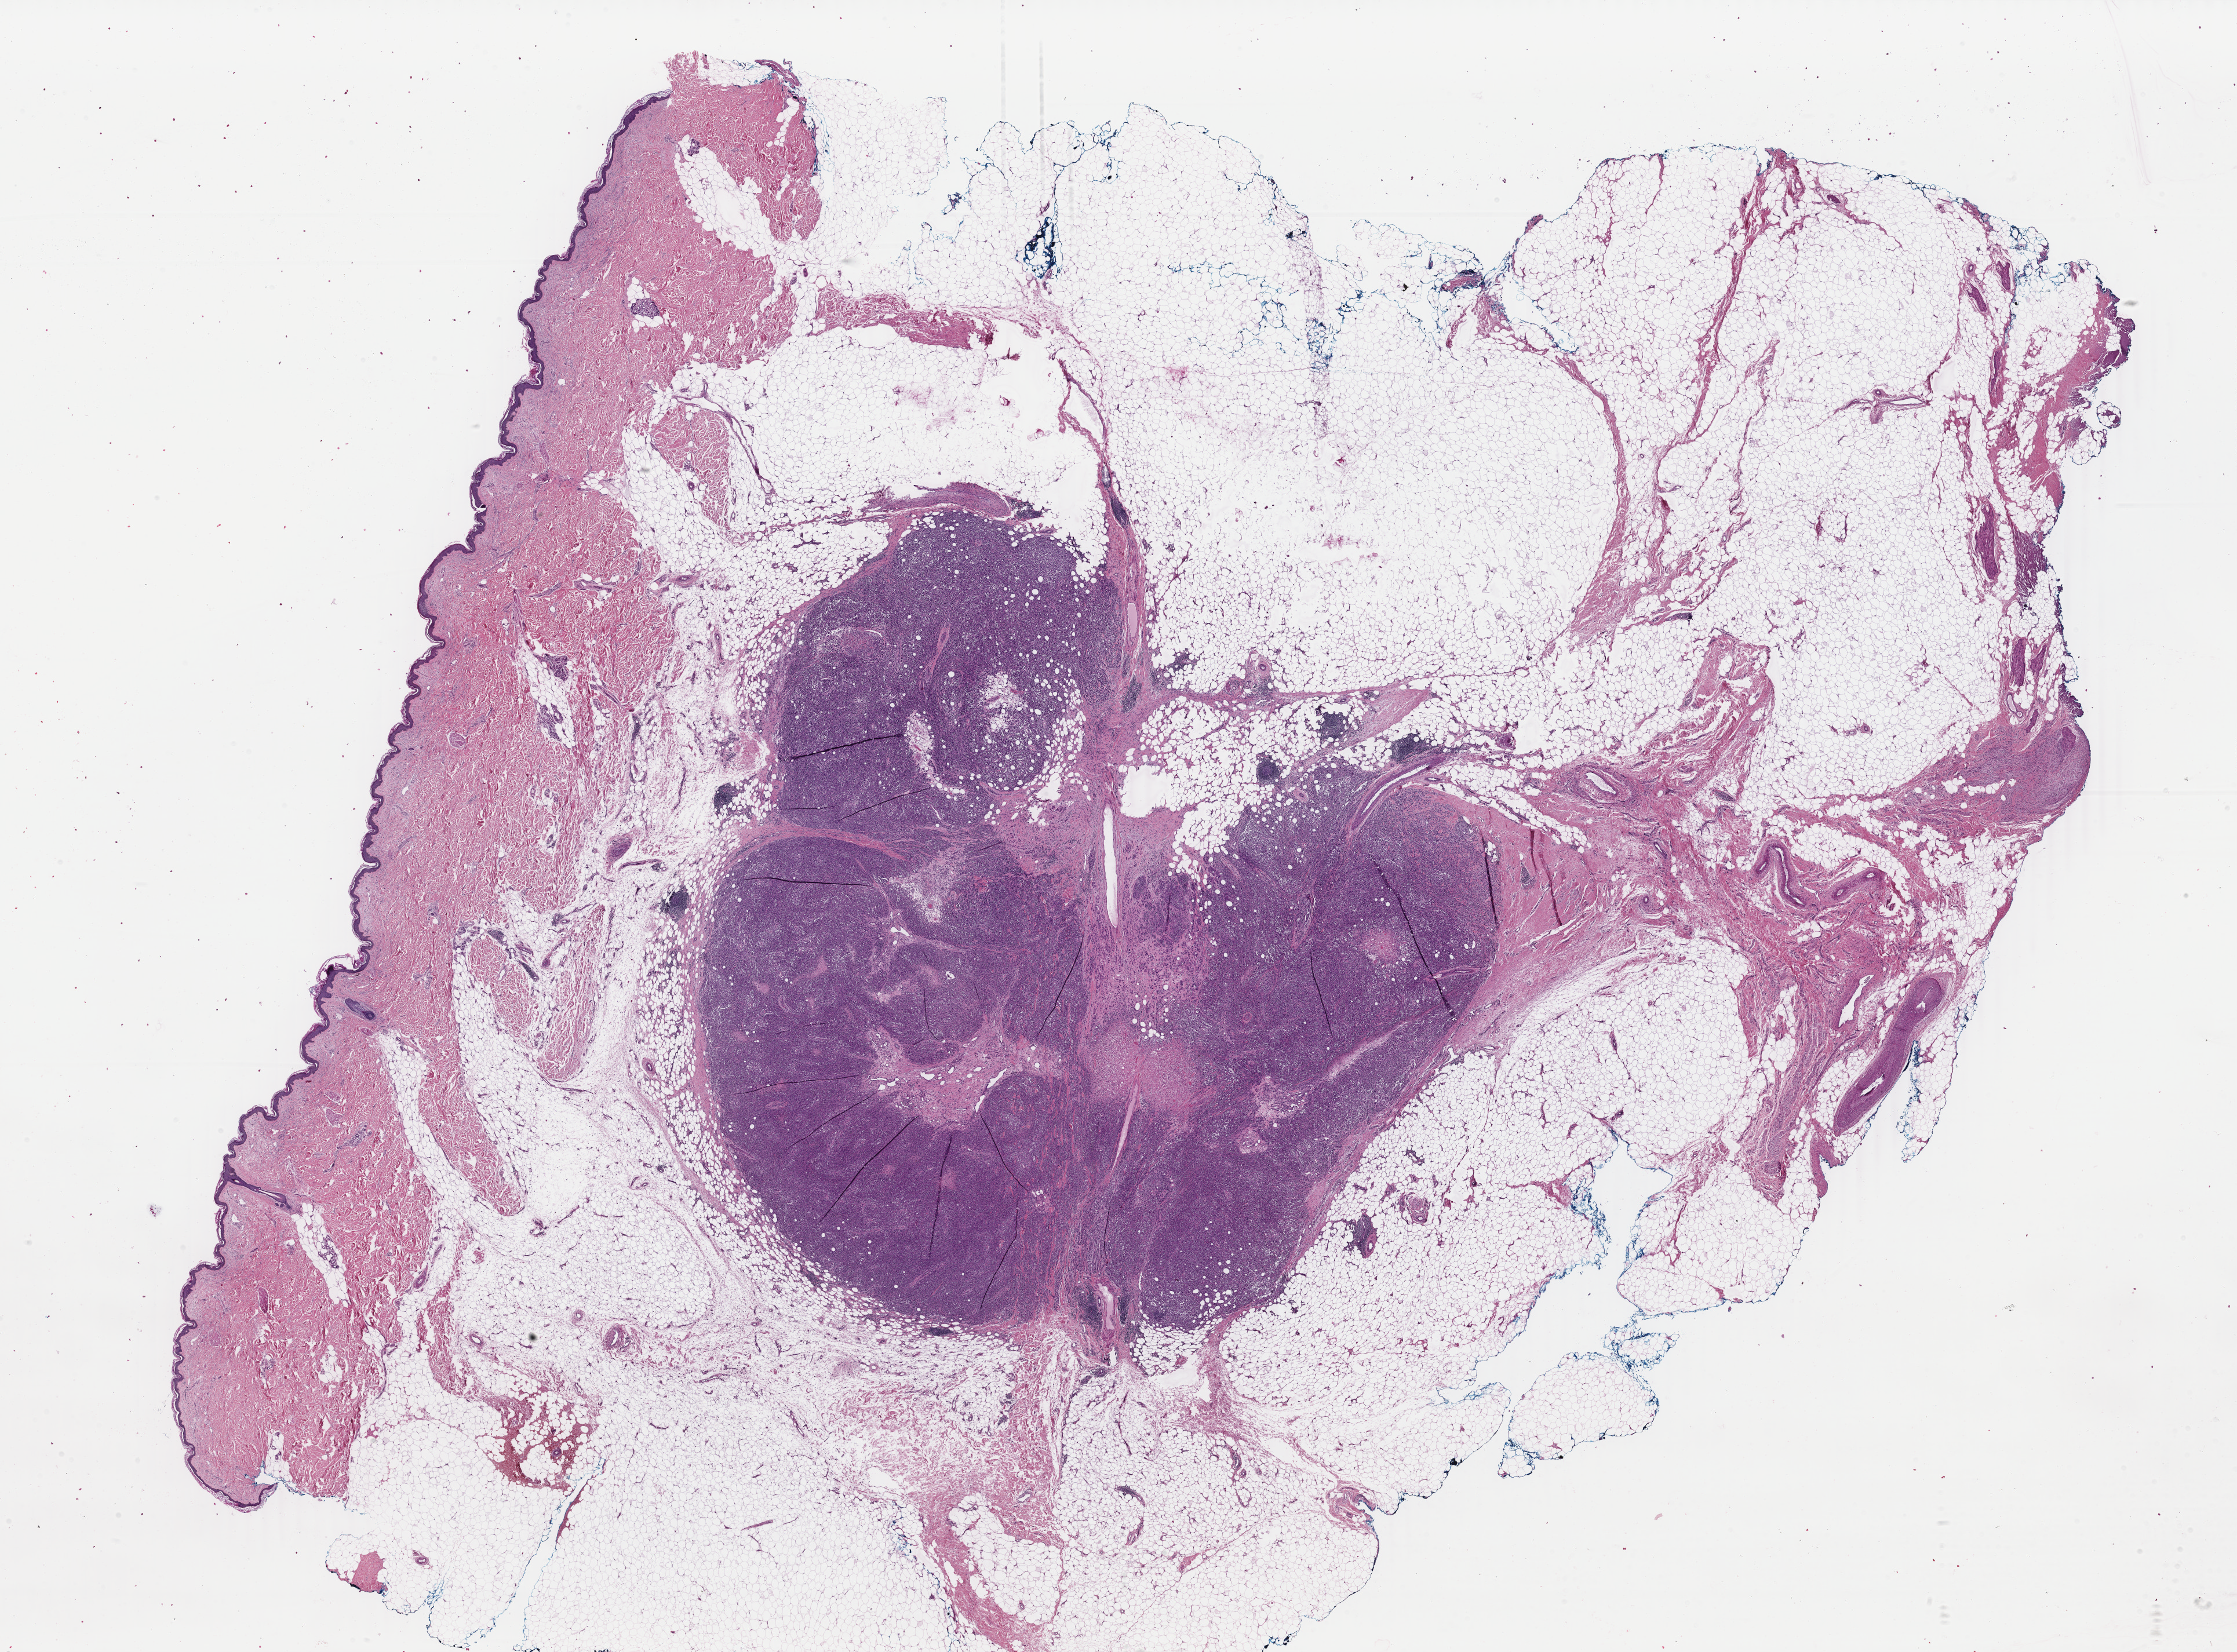
H&E-stained whole-slide image — a low-resolution overview of the entire scanned area, about 30.7 x 22.7 mm; FFPE section; primary tumour sample from the skin. Female patient; age at initial diagnosis 70 years.
Pathologic diagnosis: Malignant melanoma, NOS.